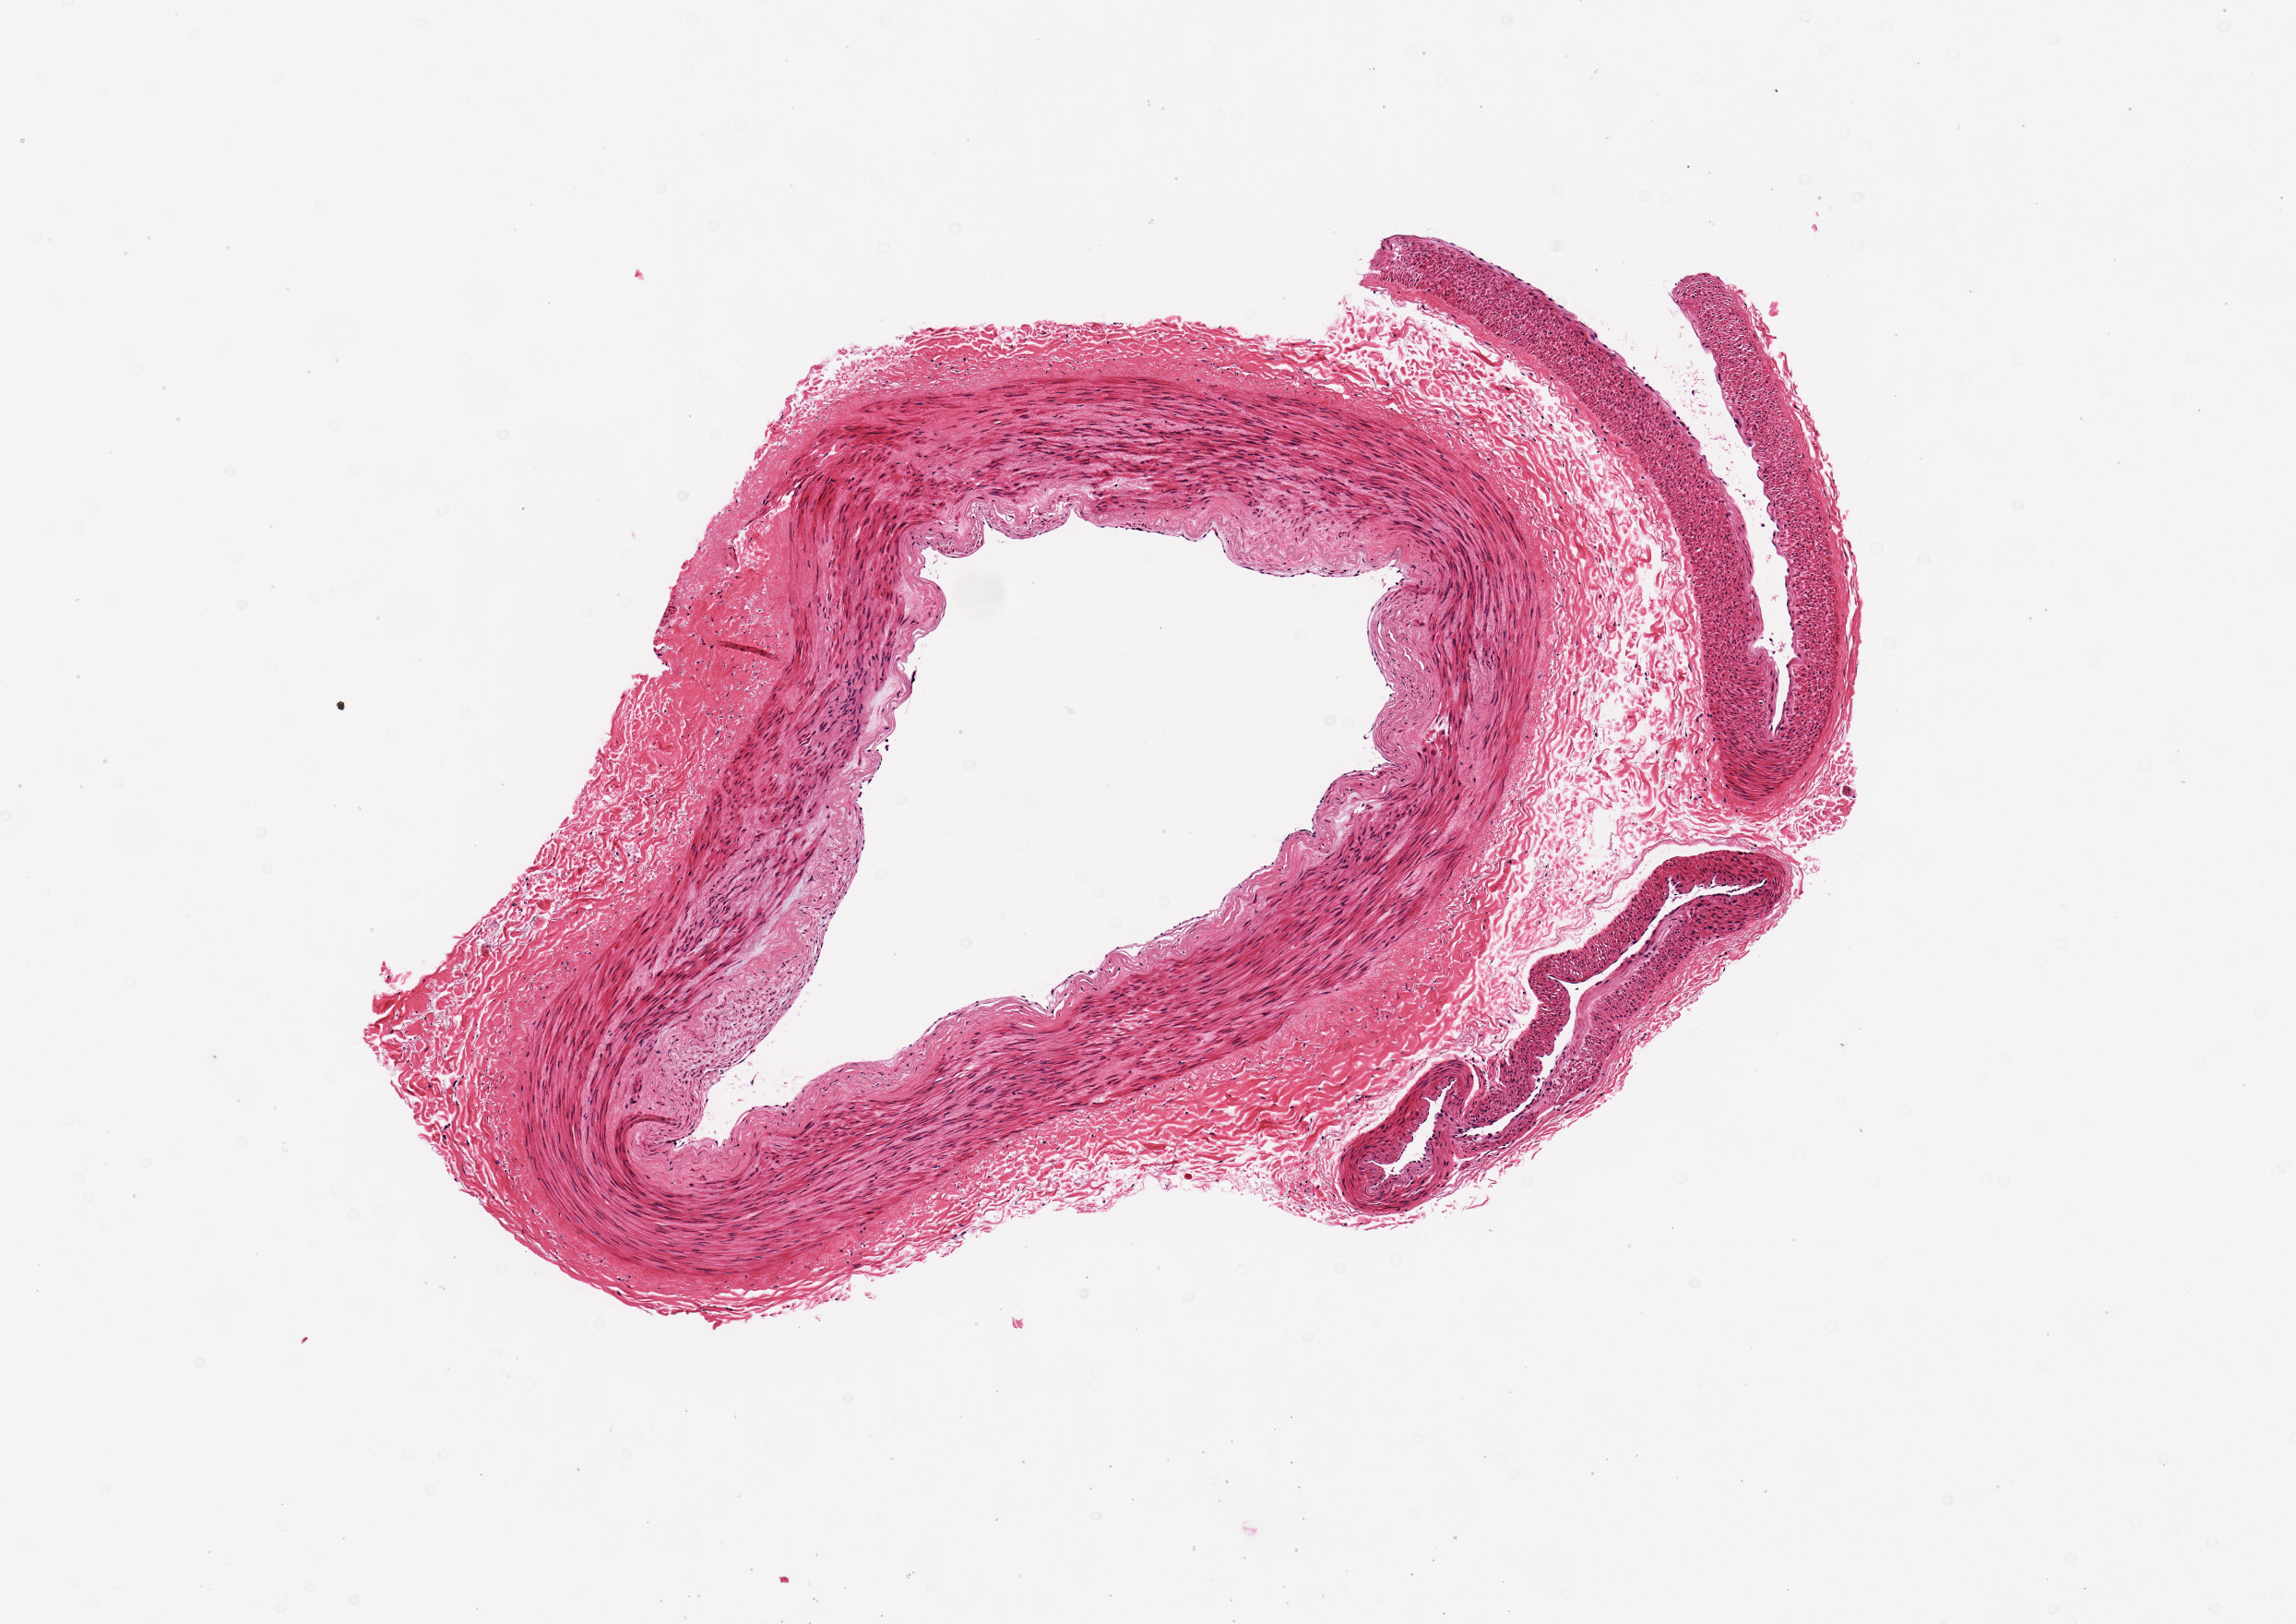
Whole-slide image, hematoxylin and eosin (H&E) stain — a low-resolution overview of the entire scanned area, about 4.9 x 3.5 mm; PAXgene-fixed, paraffin-embedded tissue; target tissue: tibial artery; tissue donor sample.
Pathologist's review note for this sample: No lesion. 3x2mm diameter.